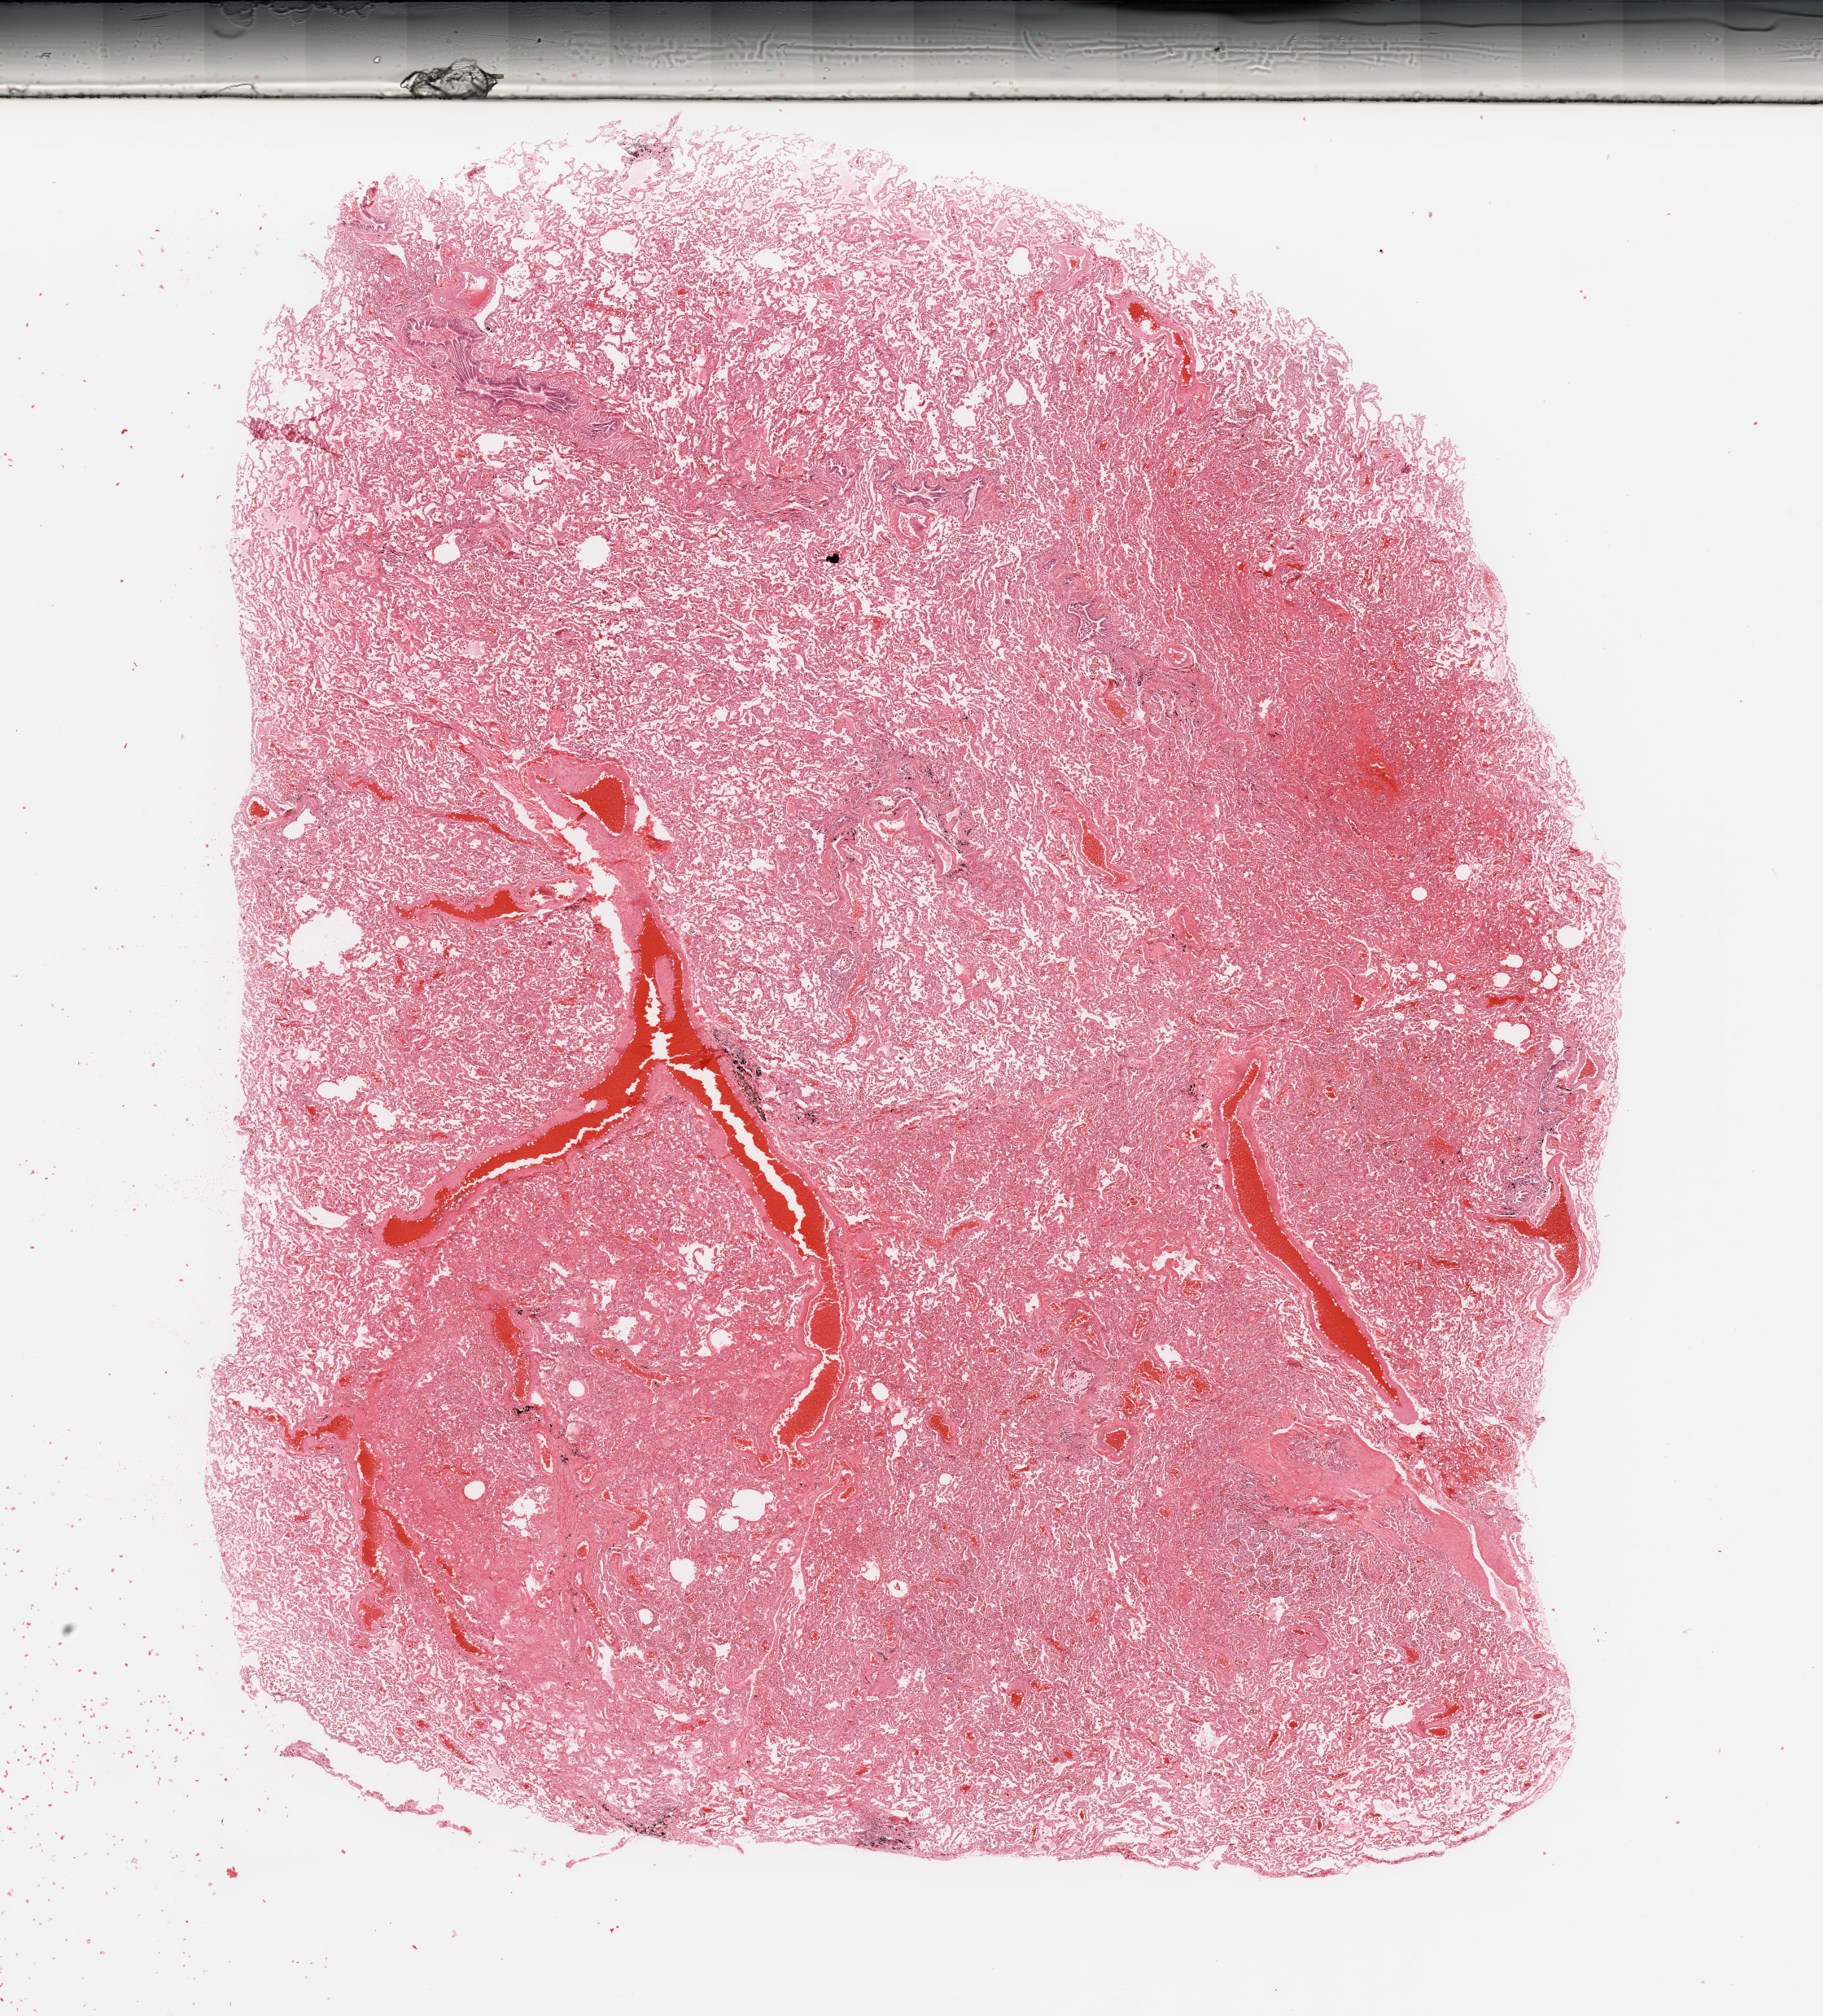
Whole-slide histology image, H&E-stained, low-resolution overview of the scanned area, about 17.7 x 19.6 mm; normal (non-tumour) tissue sample, lung. 57-year-old male patient.
* this section: normal (non-tumour) tissue from the same patient
* patient diagnosis: Adenocarcinoma, NOS